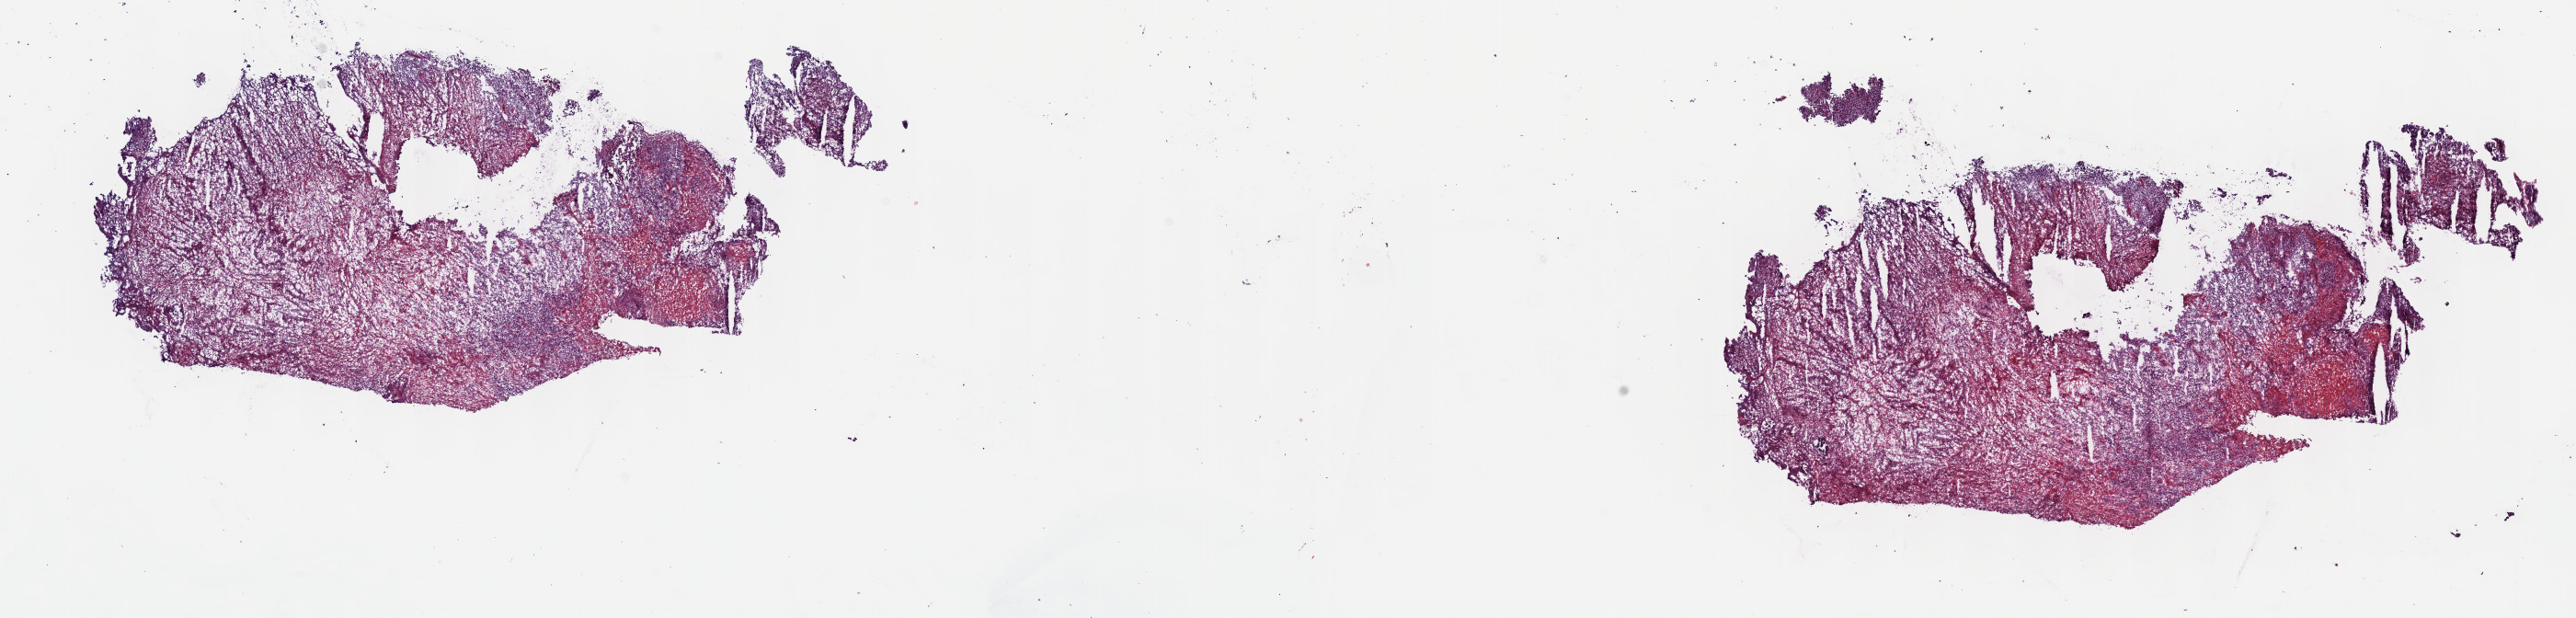
Hematoxylin and eosin (H&E) stained whole-slide image — a low-resolution overview of the entire scanned area, about 22.7 x 5.4 mm (acquisition: 40x scan), frozen section from the top of the tissue portion, primary tumour sample from the skin. Patient: female, age at initial diagnosis 73 years. Pathologist review of this section (percent, as recorded): tumour cells 100%, tumour nuclei 80%, normal cells 0%, stromal cells 0%, necrosis 0%. Infiltration values recorded for this section: lymphocyte infiltration 2%, monocyte infiltration 0%, neutrophil infiltration 0%.
AJCC pathologic stage: IIC (7th edition). Diagnosis: Amelanotic melanoma.